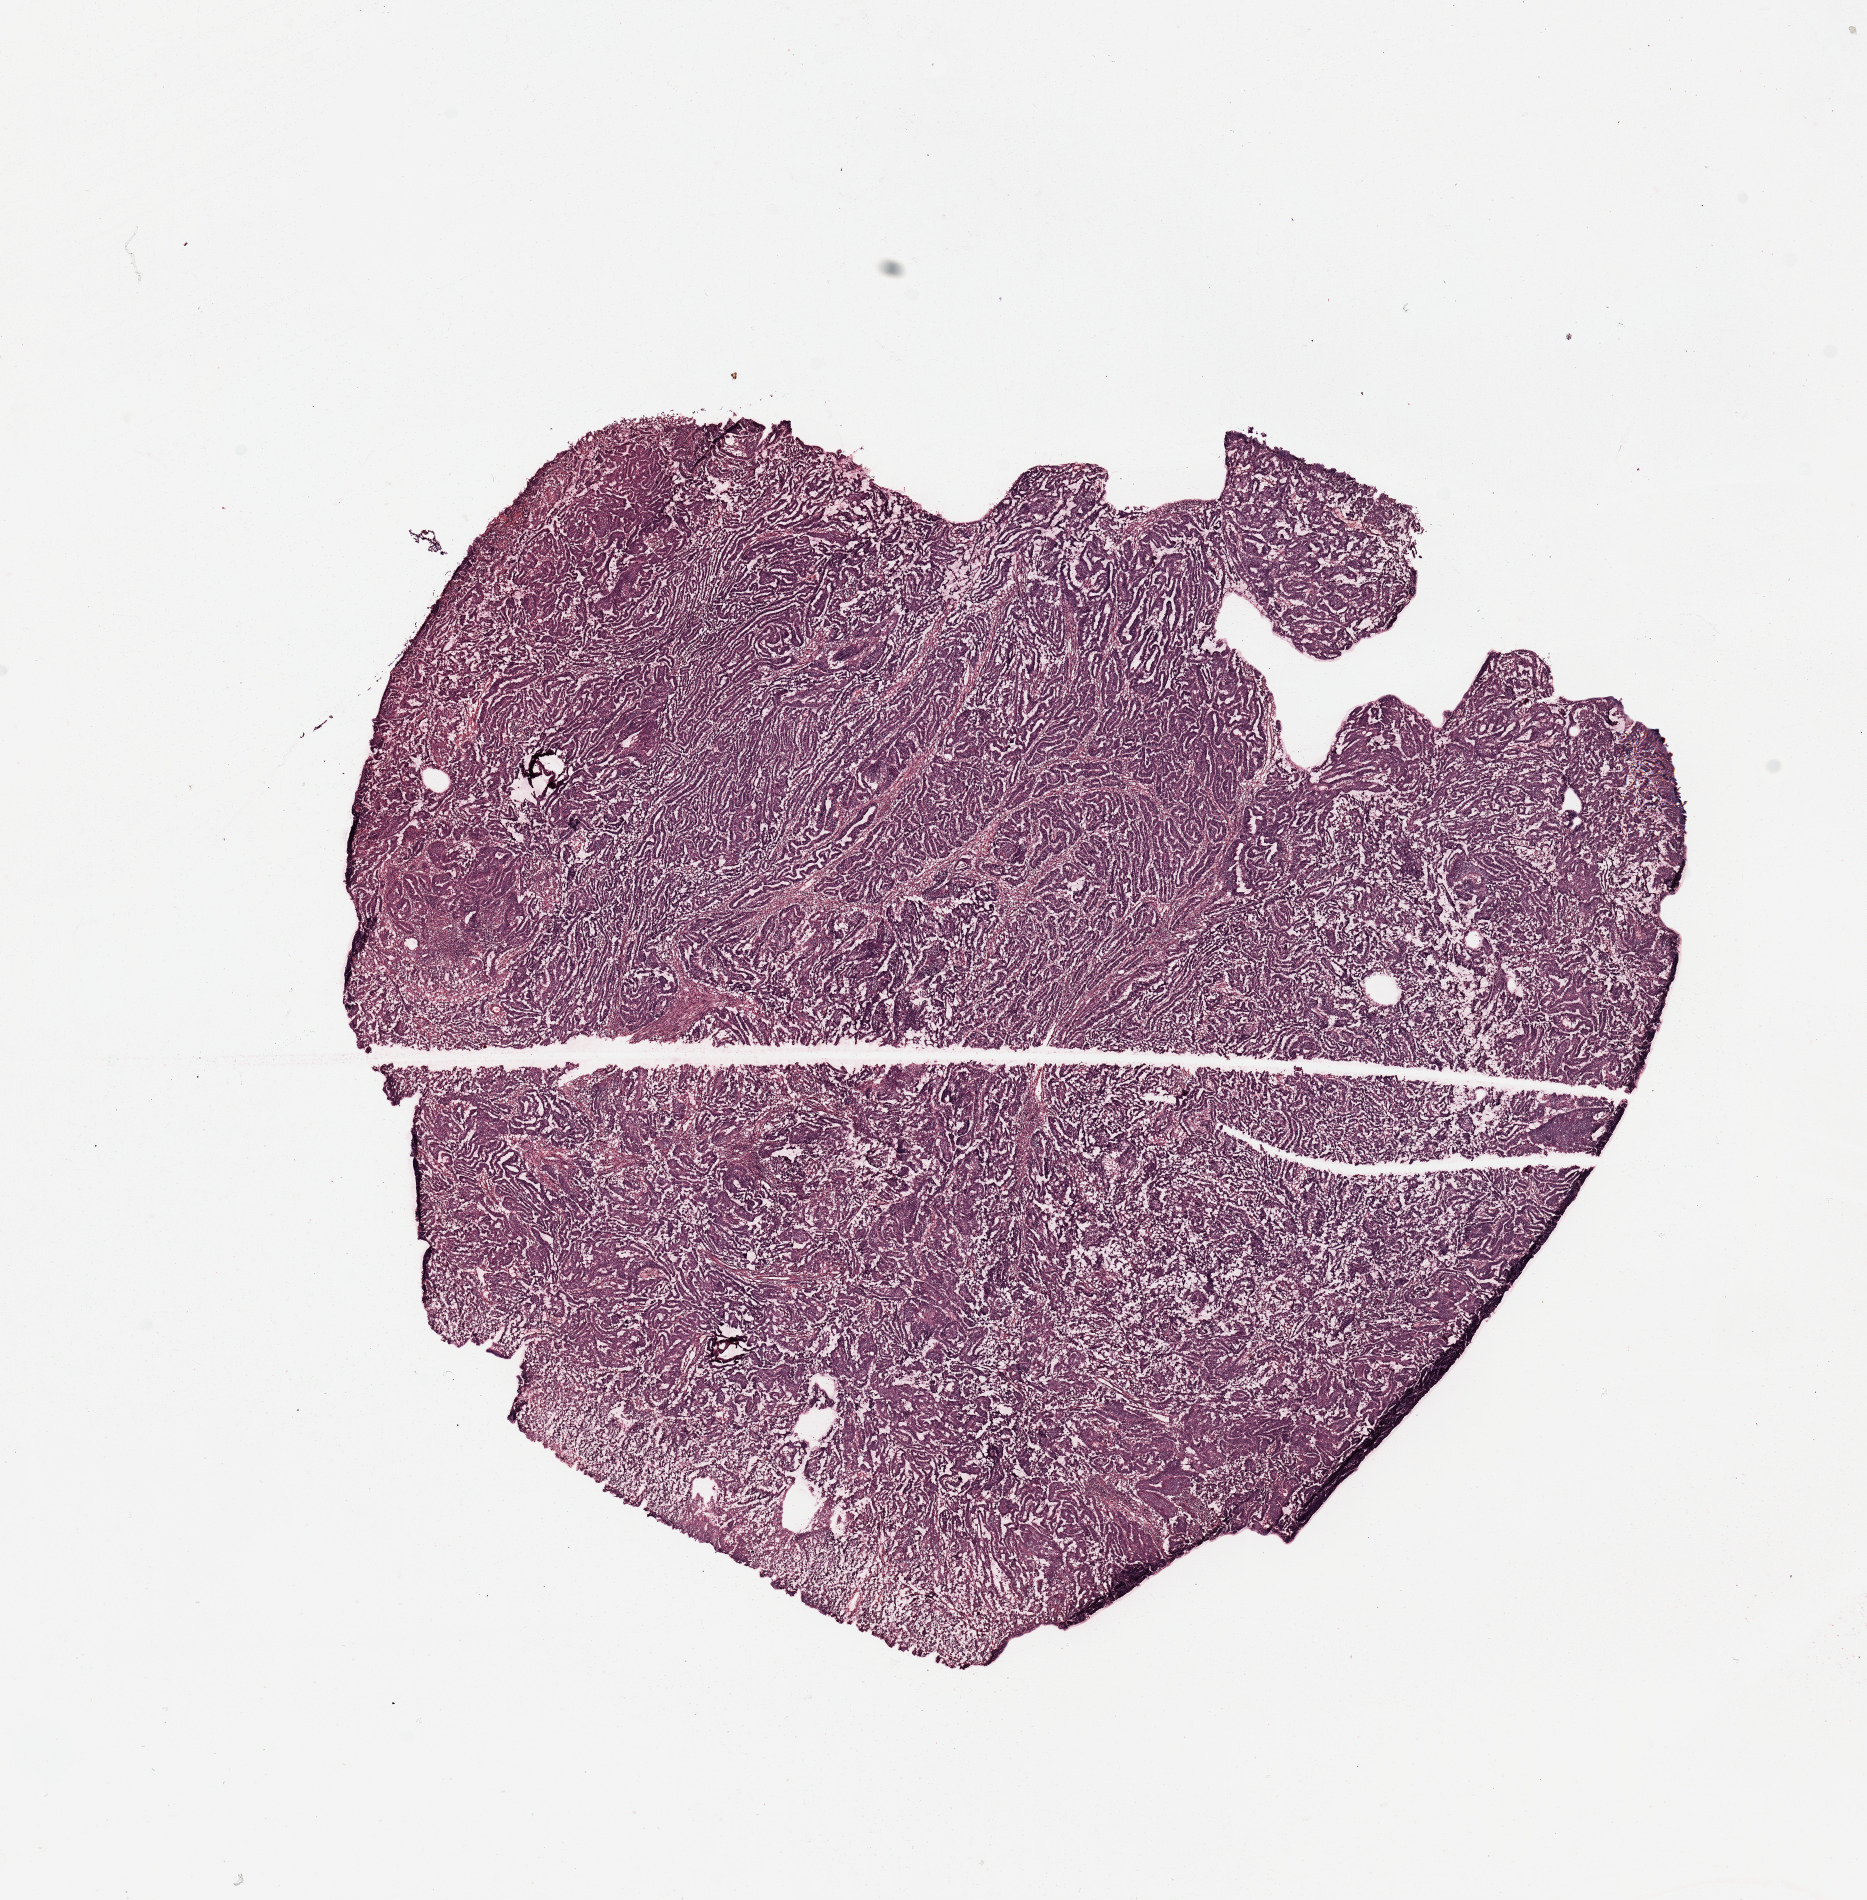
Whole-slide histology image, H&E, low-resolution overview of the scanned area, about 14.8 x 15.0 mm, tumour tissue sample, uterus. Patient: female, age 64 years. Histologic grade: G1 (well differentiated).
AJCC pathologic stage: I. Diagnosis: Endometrioid adenocarcinoma, NOS.